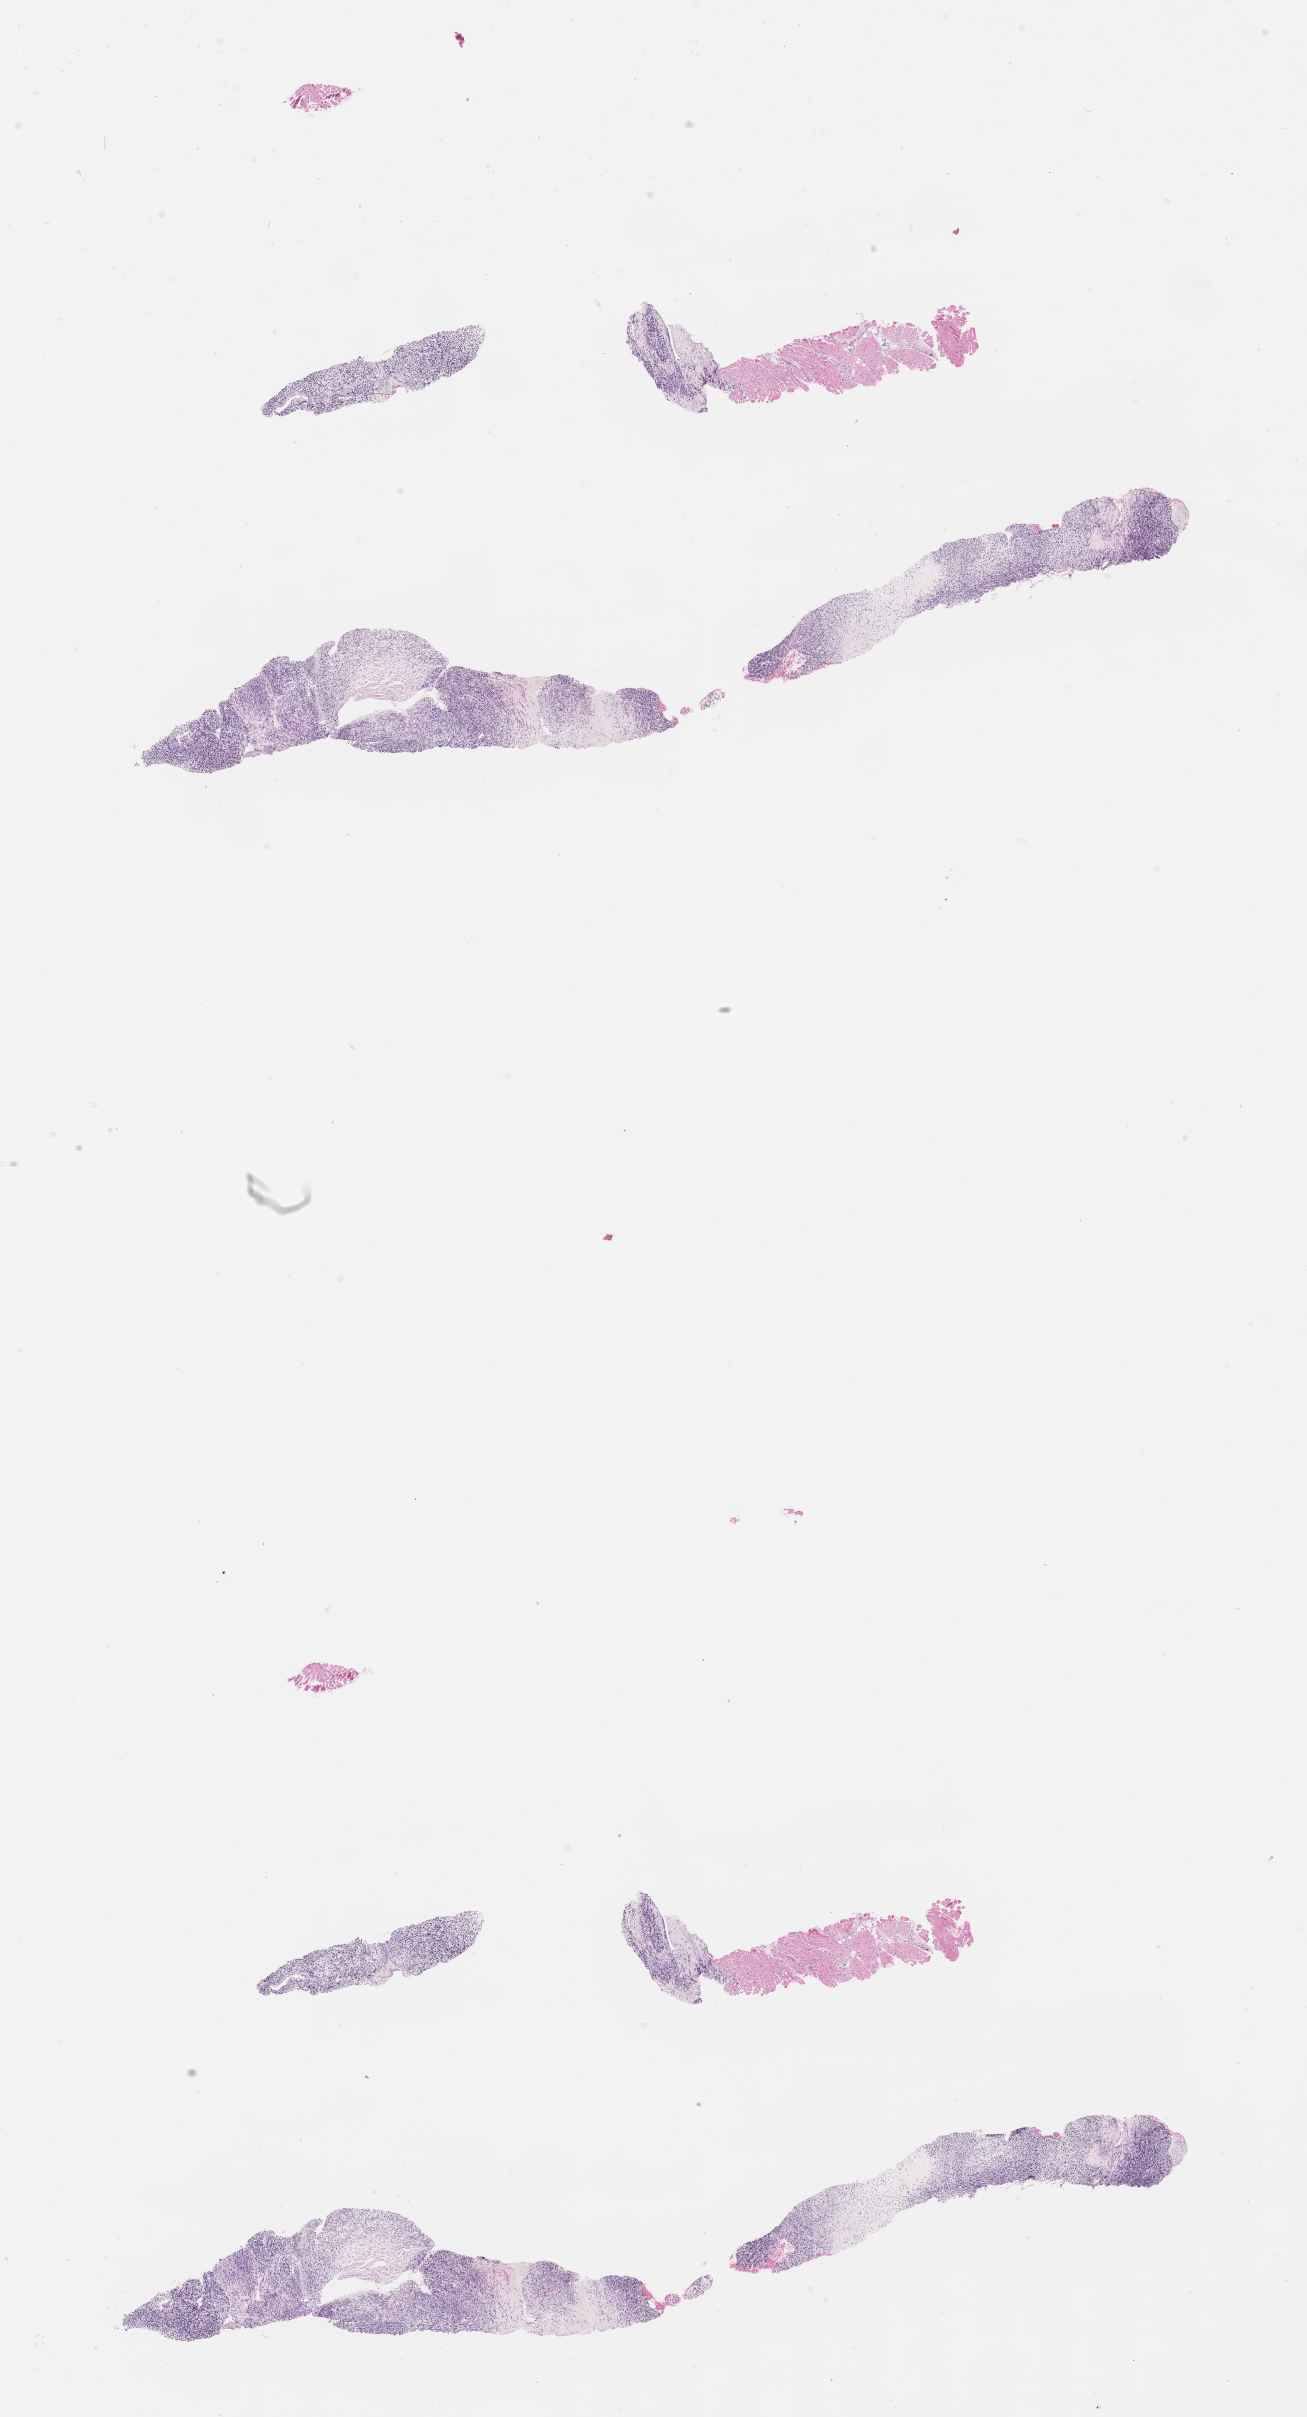
Whole-slide image, haematoxylin and eosin stain of tumor tissue, low-resolution overview of the scanned area, about 10.6 x 19.5 mm, formalin-fixed paraffin-embedded section, sample anatomic site: bone, temporal-infra. Female patient, age at diagnosis 3.3 years.
Metastatic status at presentation (as recorded): metastatic (confirmed). Diagnosis: rhabdomyosarcoma; histological classification: embryonal rhabdomyosarcoma. Stage (as recorded): 4. Primary site (case record): infratemporal fossa (PM).